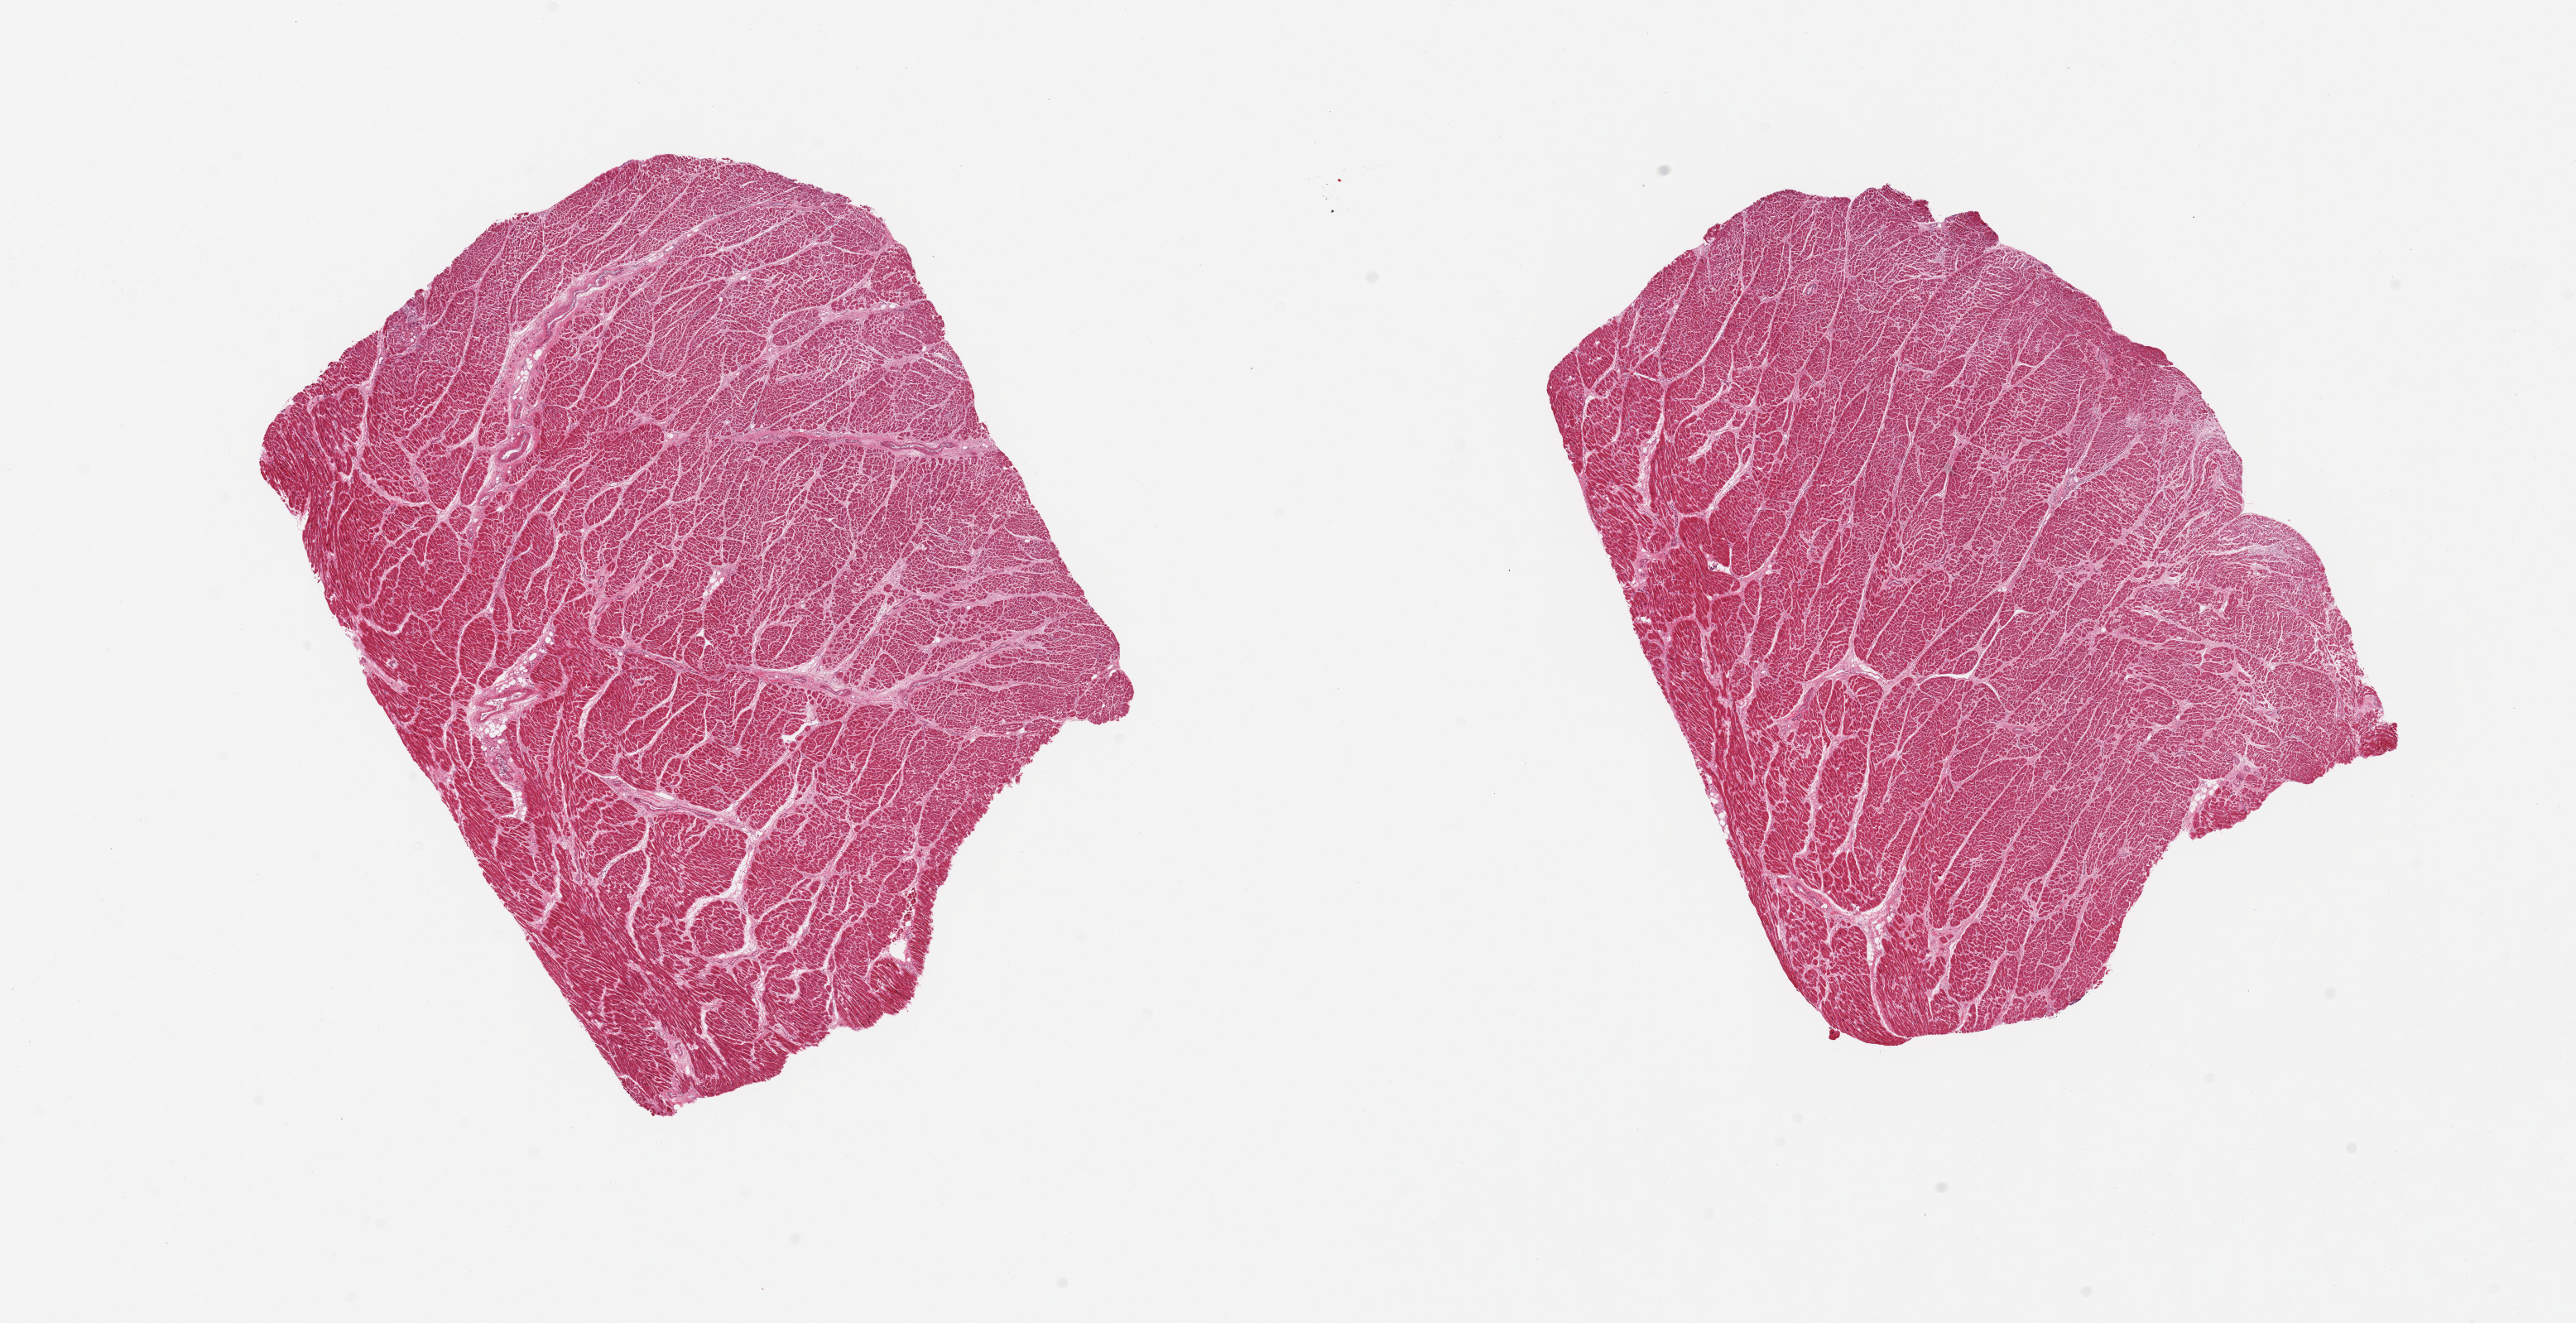
Digitized H&E-stained section, whole scanned area (about 24.6 x 12.6 mm) shown as a low-resolution overview, PAXgene-fixed, paraffin-embedded tissue, target tissue: heart, donor tissue sample. Male donor.
Review note (as recorded): 2 pieces, moderate chronic ischemic changes/interstitial fibrosis.